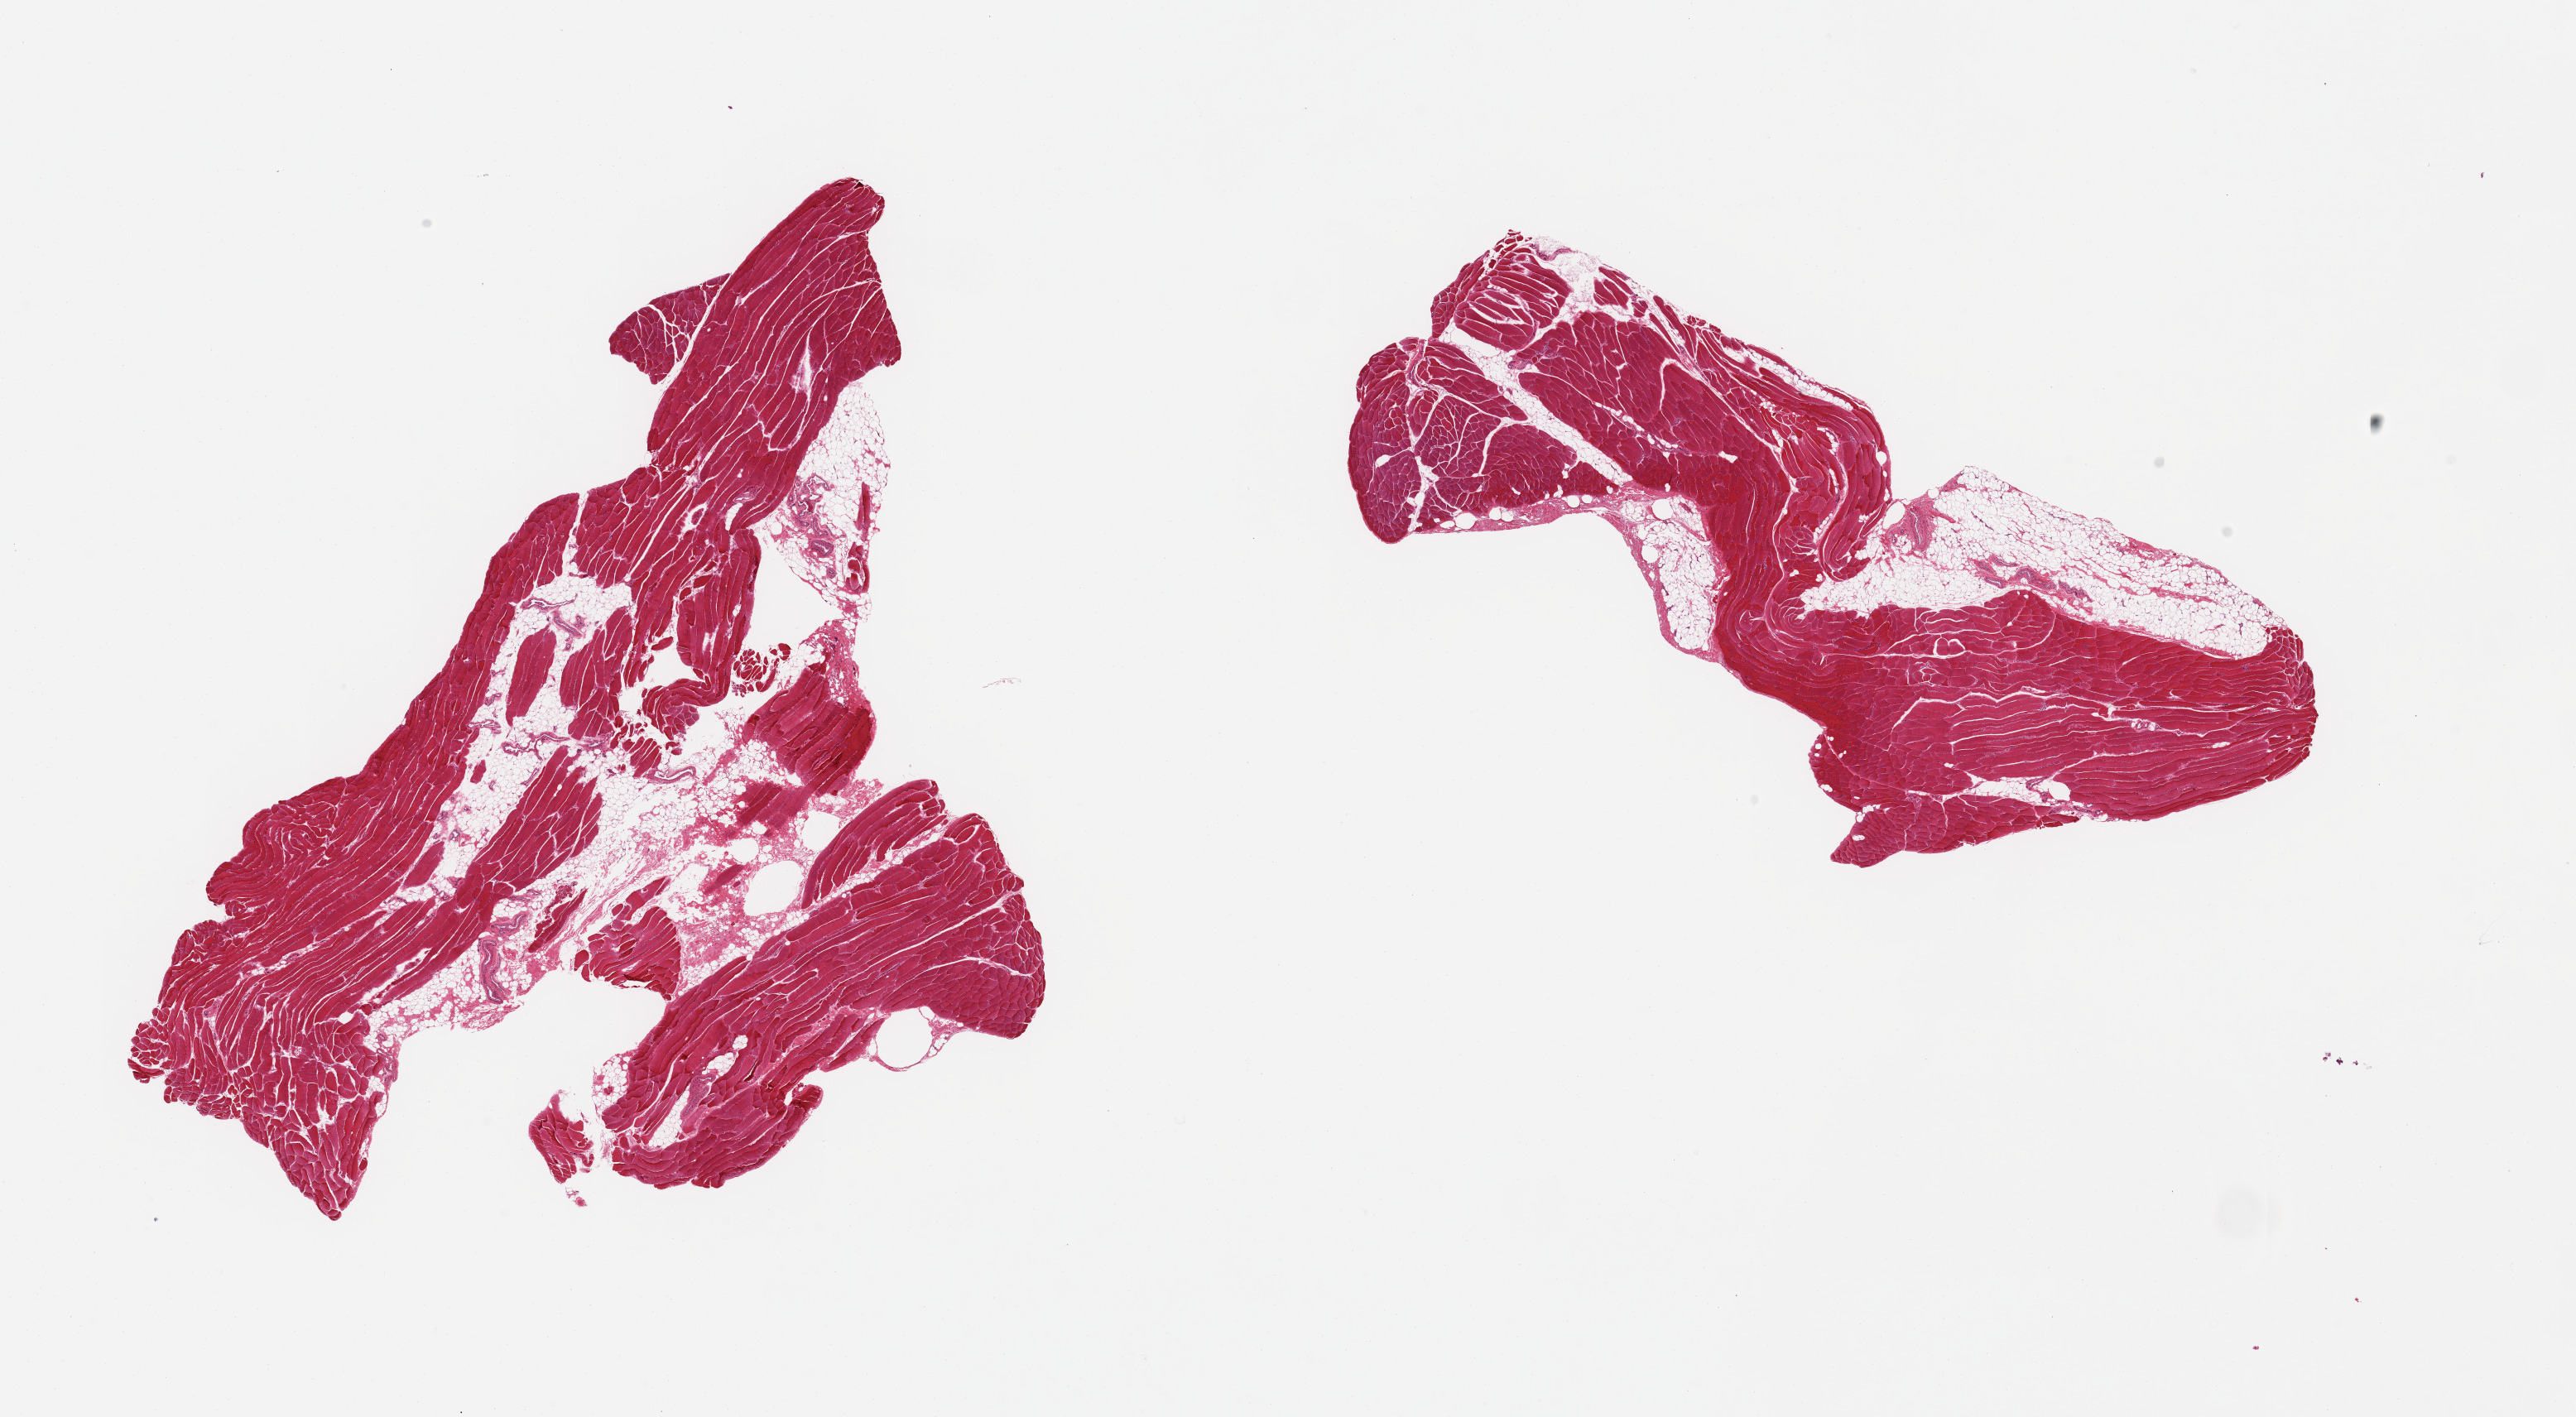
Haematoxylin and eosin whole-slide image, brightfield — low-resolution overview of the scanned area, about 24.6 x 13.5 mm (acquisition: 20x scan); PAXgene-fixed paraffin-embedded (PFPE) section; section of skeletal muscle (target tissue); donor tissue sample. Donor sex: male.
Reviewer comment on this tissue sample: 2 pieces, 20% interstitial fat/vascular elements.